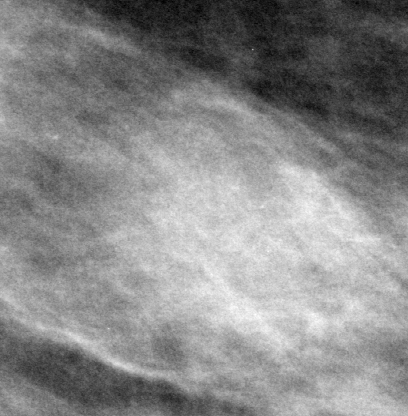
Region of interest cut from a scanned film mammogram (one marked finding), left breast, MLO view.
- Marked abnormality: mass, shape lobulated, margins ill defined; BI-RADS assessment category 4; subtlety rating 4 on a 1 (subtle) to 5 (obvious) scale; pathology (as recorded): malignant.